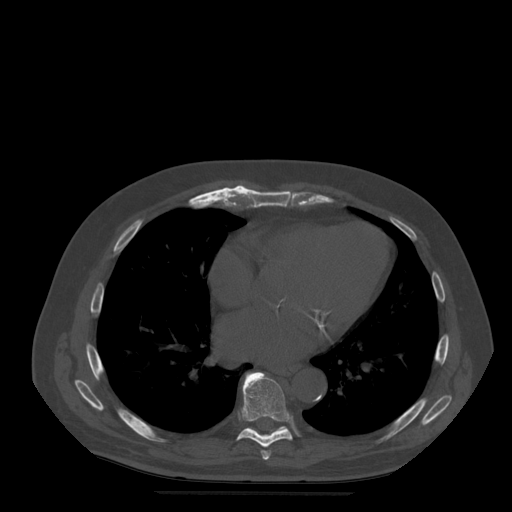
CT including the spine, one axial slice; slice 309 of 522 in the series (ordered by position); bone window (W 1800 / L 400 HU); 1.25 mm slice thickness; 512 × 512 image matrix. Patient age 72 years. From the clinical record (not read from this slice): primary cancer: prostate.
Annotated regions visible in this slice (semi-automatically segmented with operator editing):
- T7 vertebra: bounding box <261,451,271,460> (left, top, right, bottom; pixels)
- T8 vertebra: <237,372,293,448>
- T9 vertebra: <246,374,288,433>